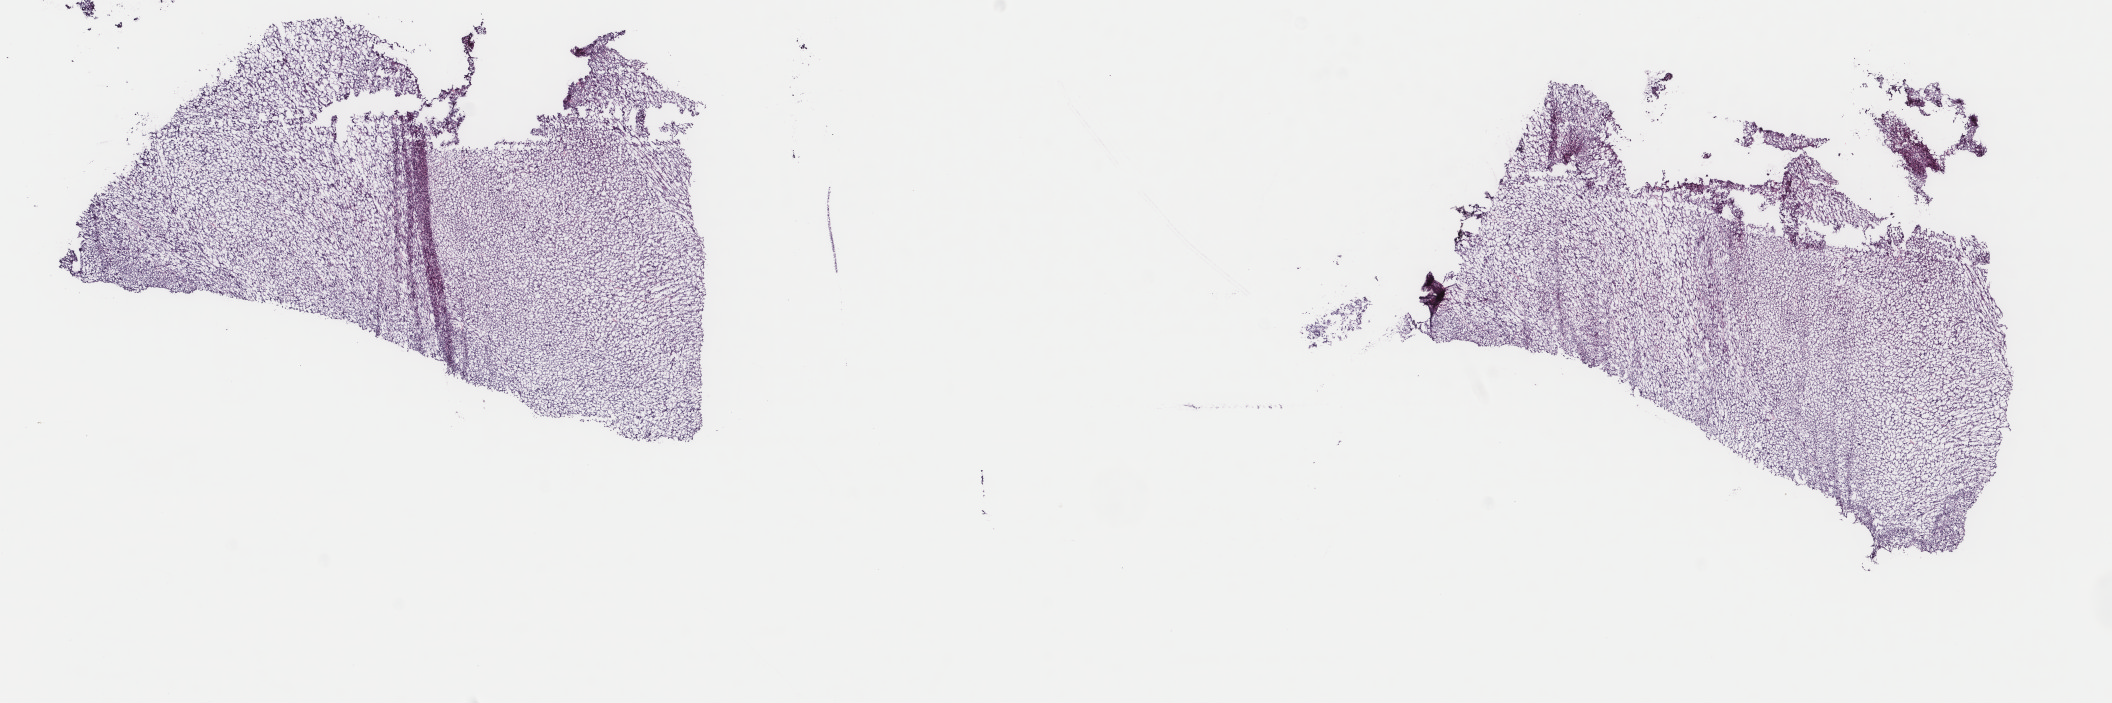
Whole-slide histology image, Hematoxylin and eosin (H&E) stained — whole scanned area (about 16.8 x 5.6 mm, slide scanned at 40x) shown as a low-resolution overview, frozen section from the top of the tissue portion, retroperitoneum and peritoneum, primary tumour sample. Female, age 53 years at initial diagnosis.
Pathologic diagnosis: Leiomyosarcoma, NOS.